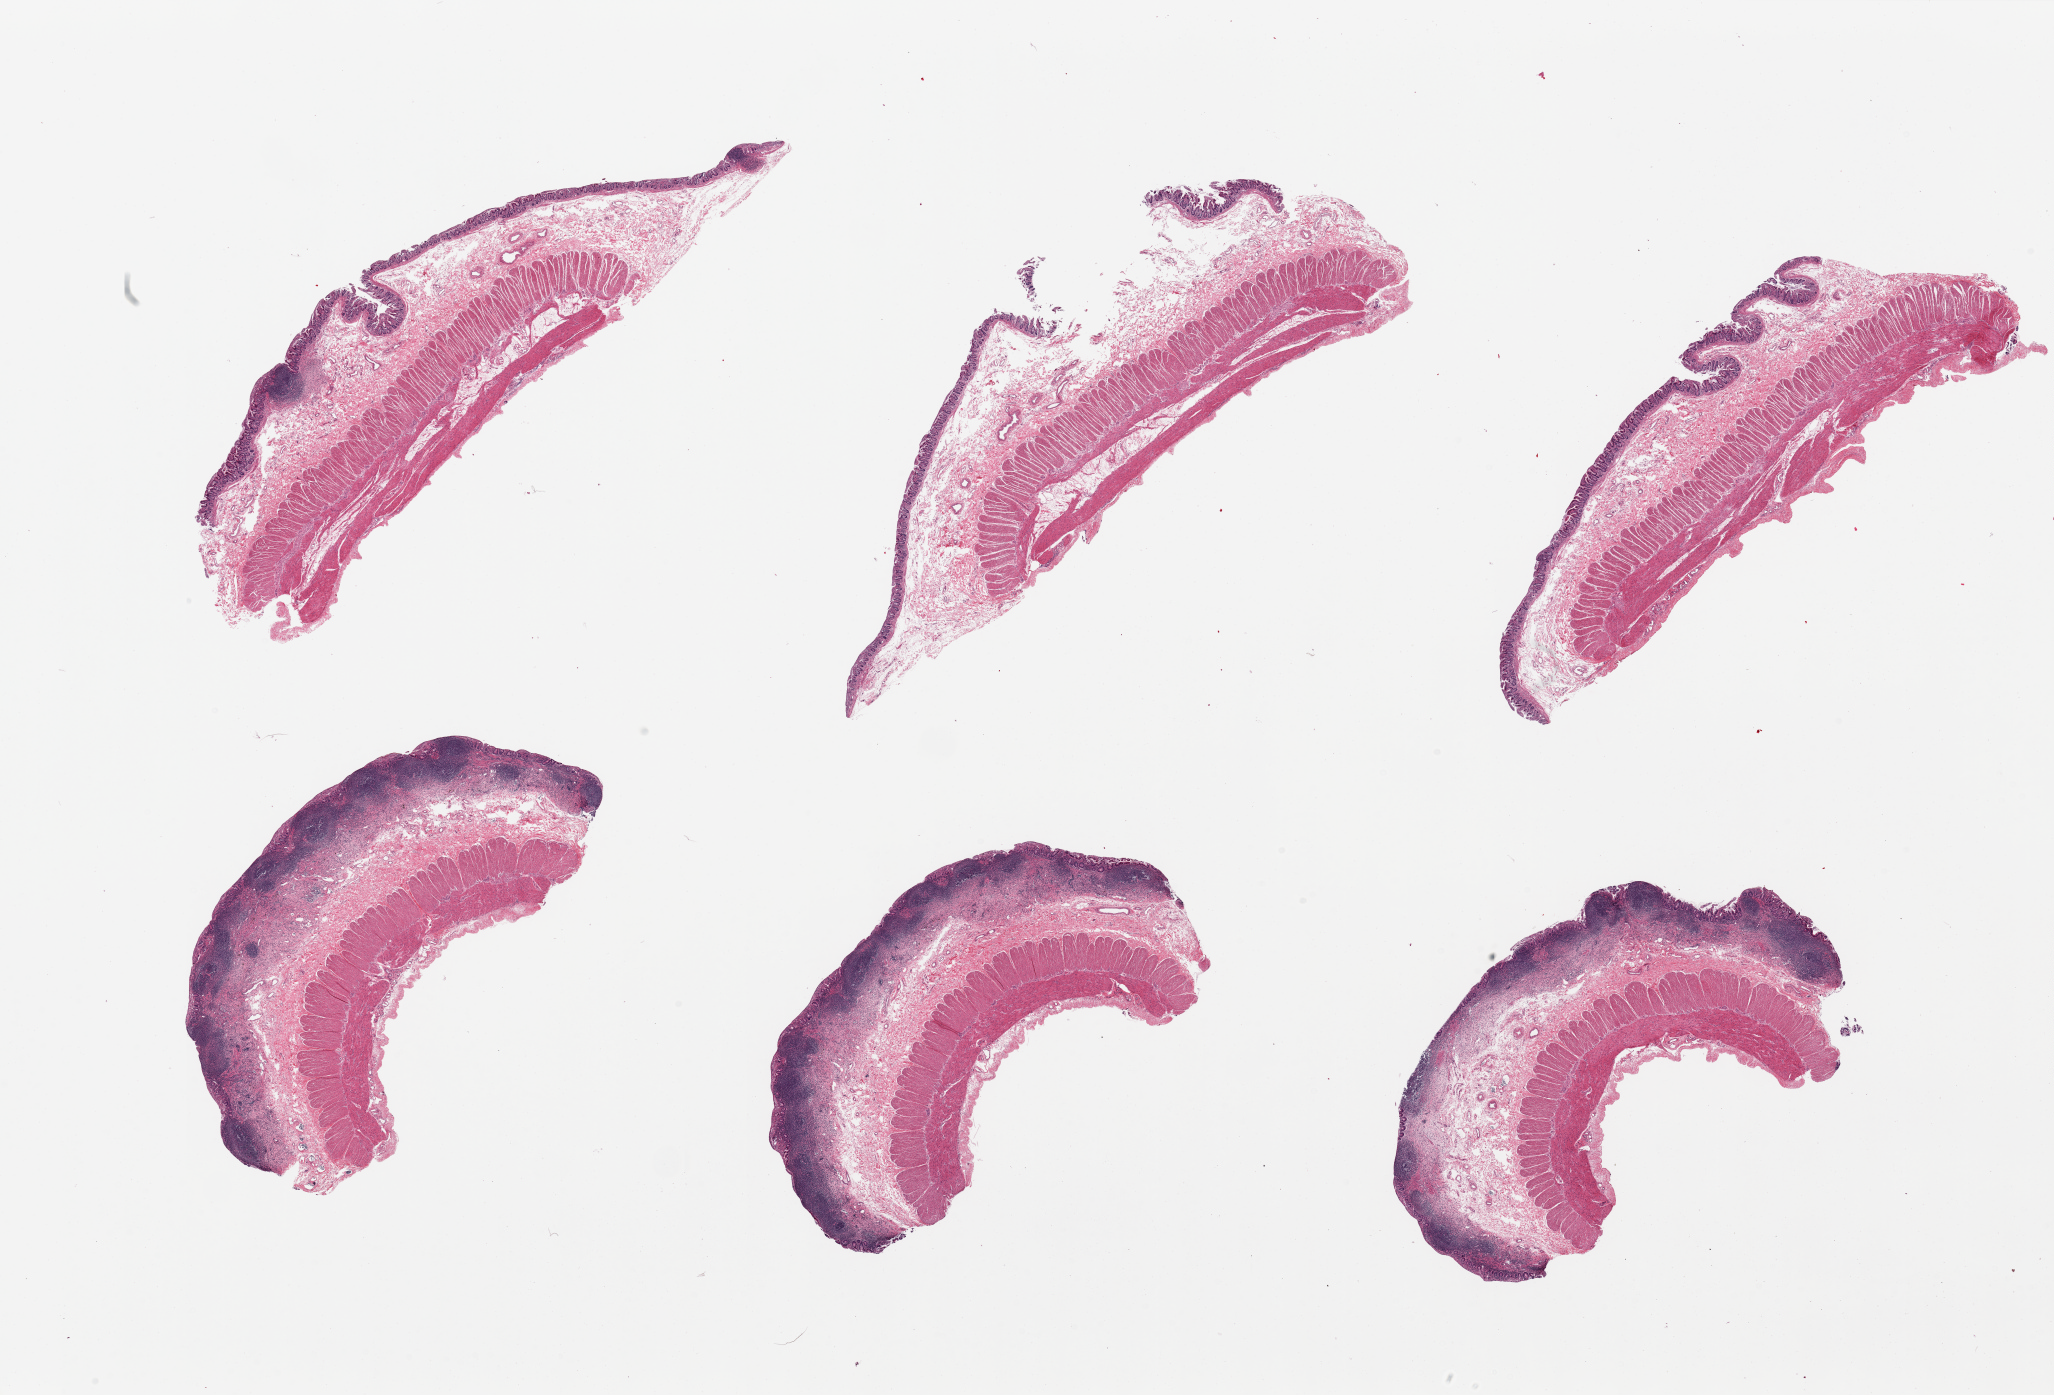
Hematoxylin and eosin (H&E) whole-slide image, brightfield, shown as a low-resolution overview of the whole scanned area (about 32.5 x 22.1 mm); PAXgene-fixed paraffin-embedded (PFPE) section; sampled site (target tissue): ileum; donor tissue sample.
* reviewer comment on this tissue sample: 6 pieces, abundant lymphoid aggregates, ~15-20% tissue present, well preserved